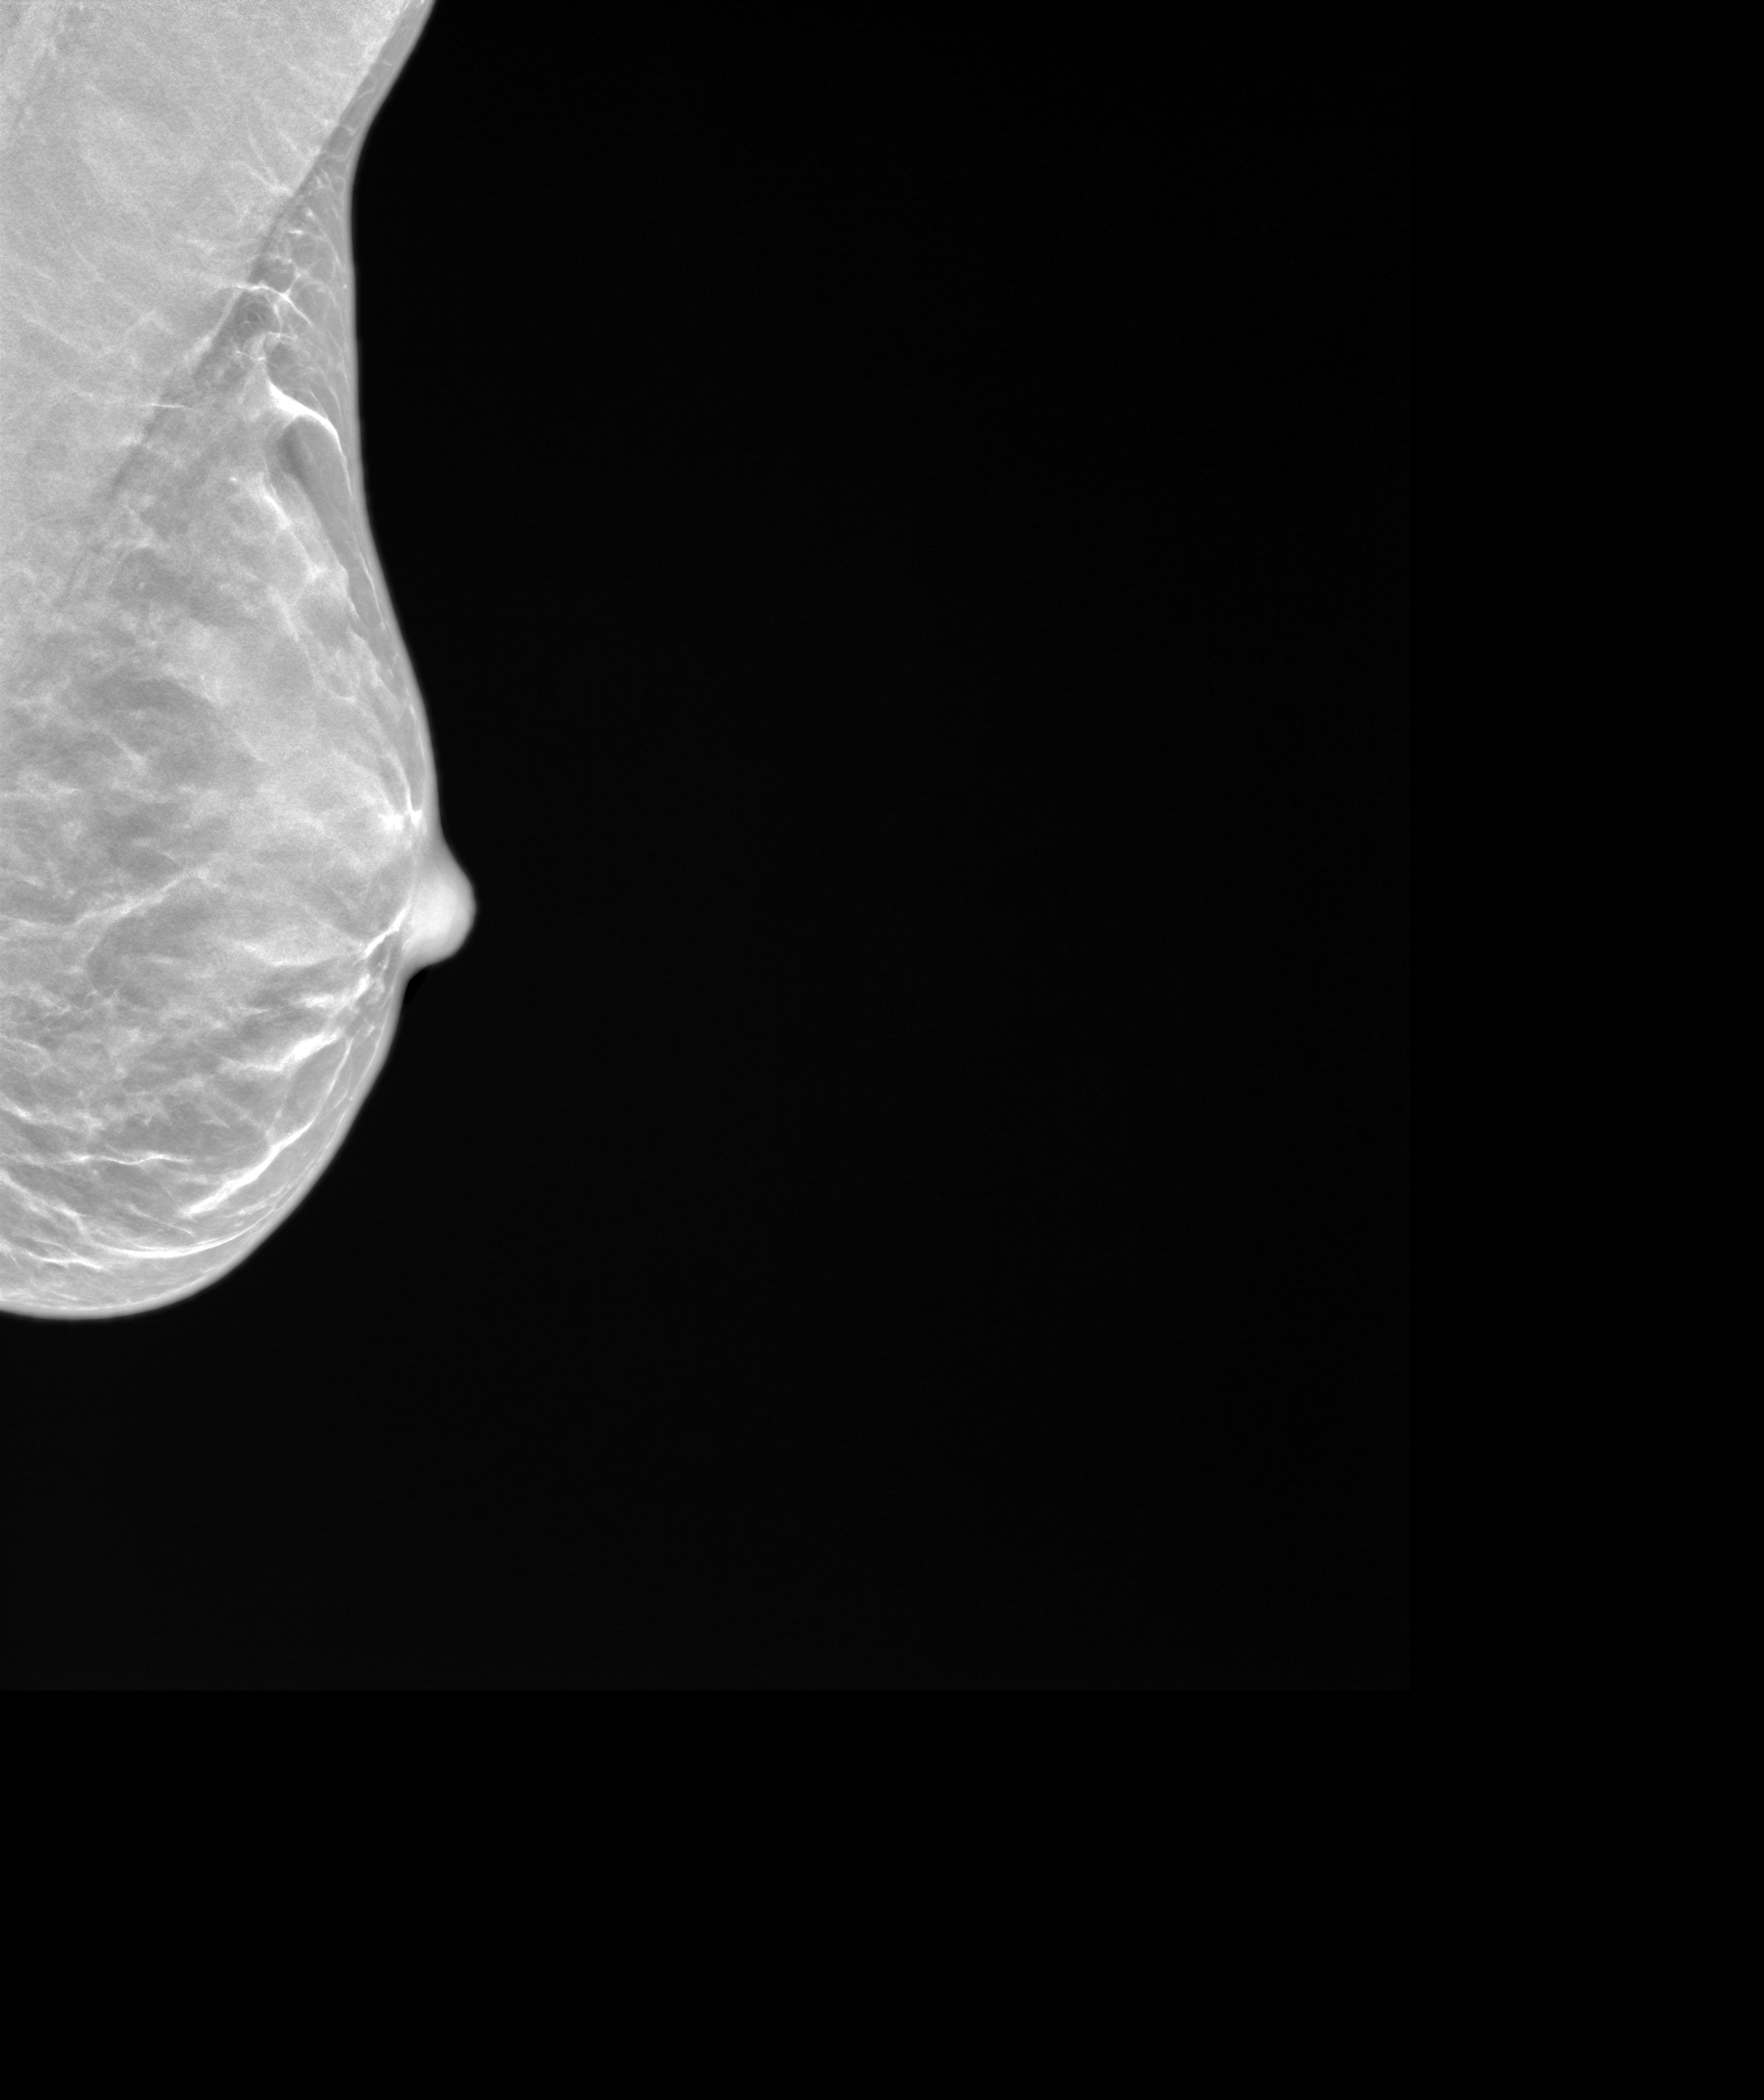
Synthesized 2-D mammogram reconstructed from digital breast tomosynthesis, left breast, mediolateral oblique (MLO) view, annual screening mammography examination. Female patient, age 54 years.
Final BI-RADS category for the screening round (tomosynthesis exam, both breasts): category 1.